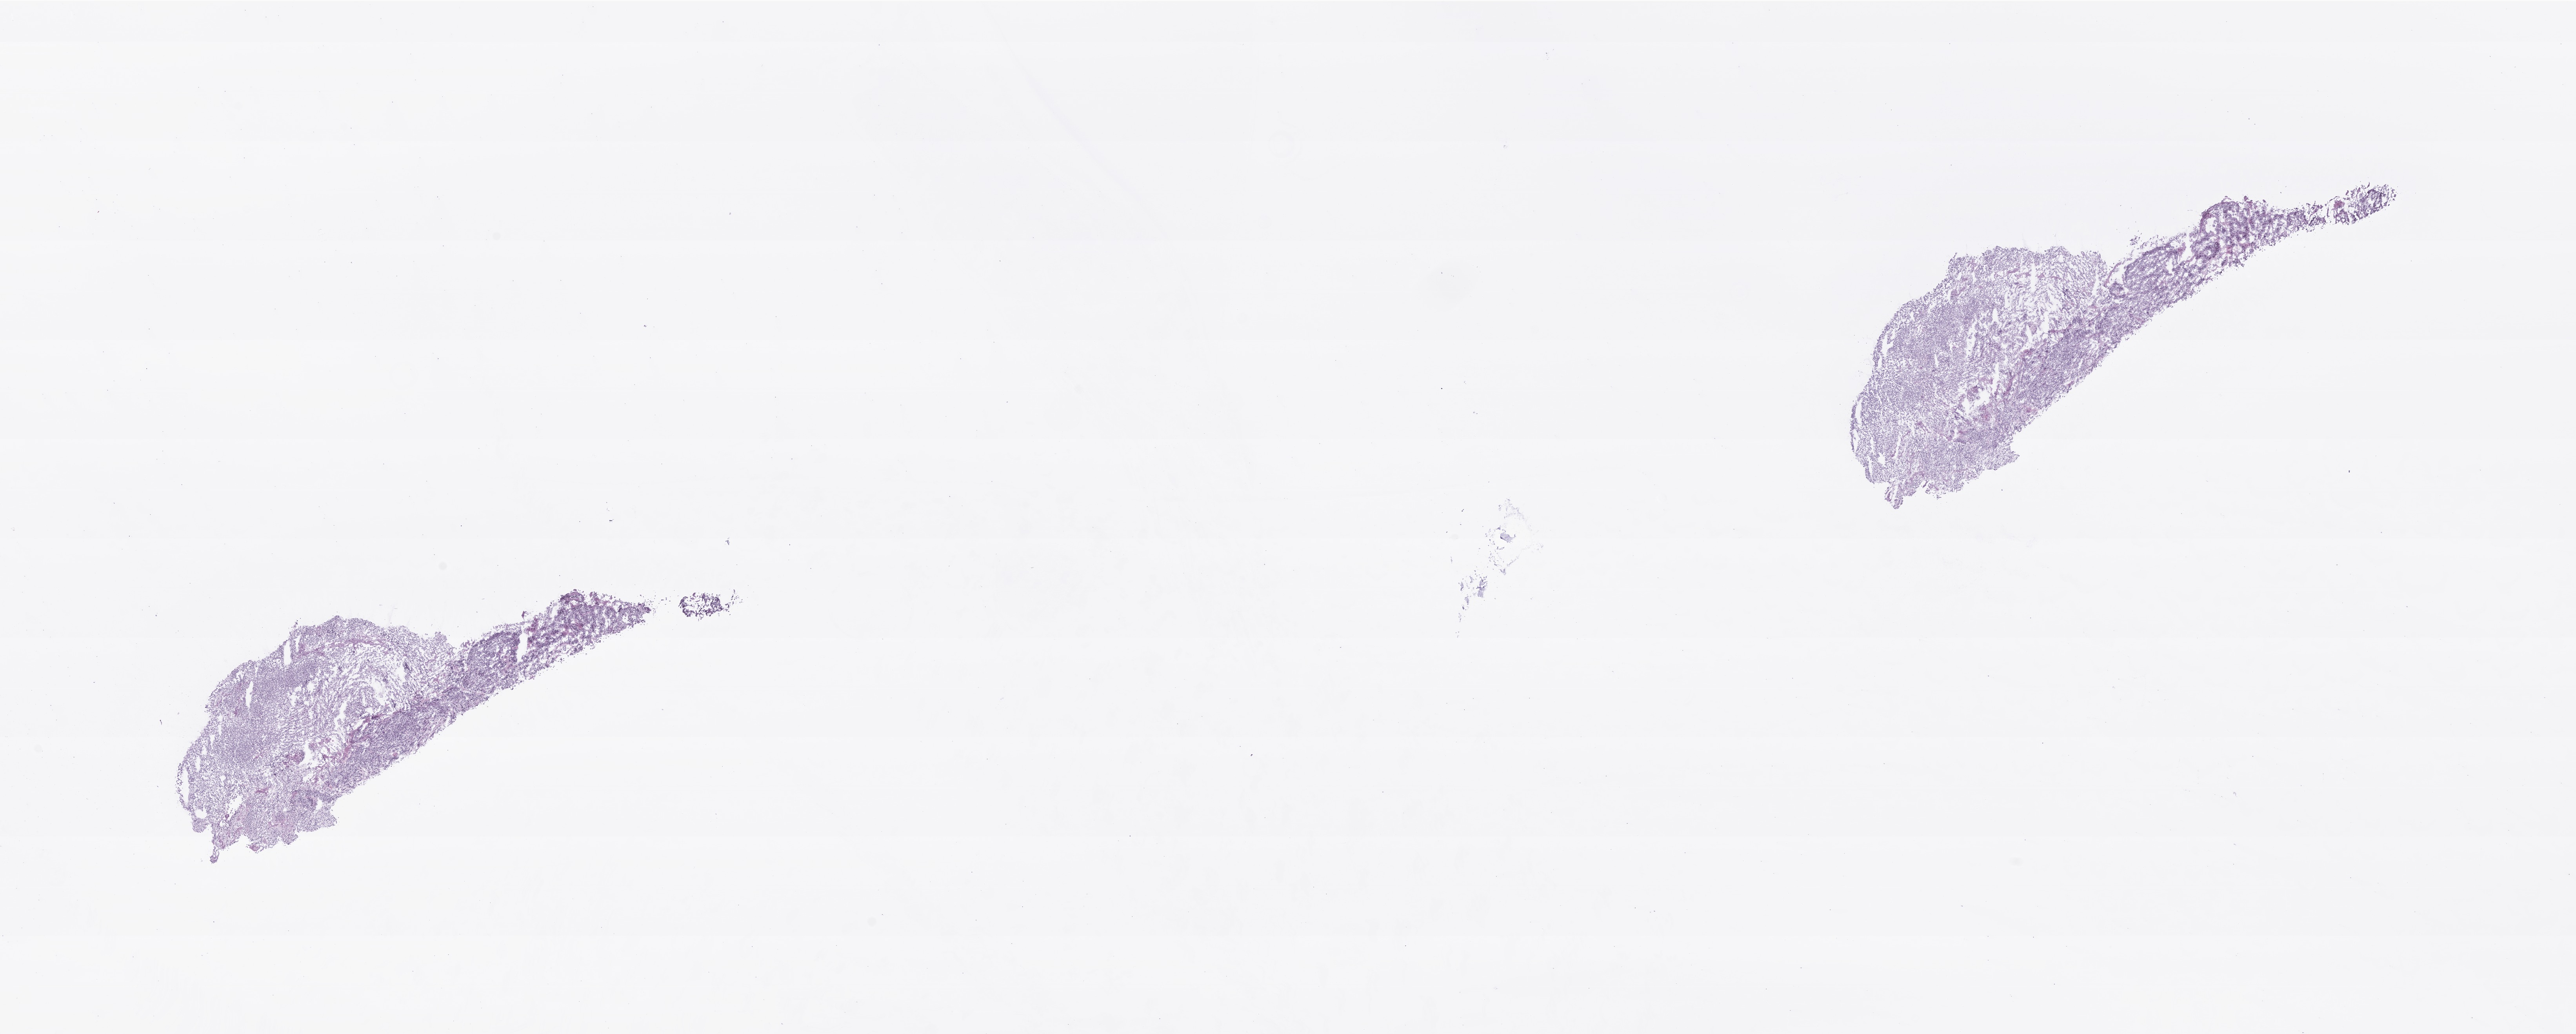
Hematoxylin and eosin (H&E) whole-slide image of tumor tissue from the cerebellum, low-resolution overview of the scanned area, about 27.6 x 11.1 mm. Frozen section. Female patient, age 166 months.
Recorded diagnosis: Medulloblastoma, NOS.